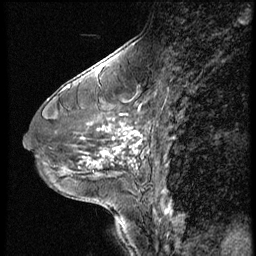
Breast MRI (dynamic contrast-enhanced), one sagittal slice. Slice 24 of 56 in the series (ordered by position). Dynamic contrast-enhanced series, image 2 of 3 at this slice position (ordered by acquisition). 1.5 T. TE 4.2 ms, TR 9 ms. 2.5 mm slice thickness. 256 × 256 image matrix, field of view 180 × 180 mm. Patient: female, 46 years. From the clinical record (not read from this slice): setting: breast cancer imaged before/during neoadjuvant chemotherapy; receptor status: HER2-positive.
Annotated regions visible in this slice (semi-automatic segmentation, software-assisted and operator-edited):
- analysis volume of interest (the breast-tissue region the enhancement analysis was run in; not a lesion): bounding box (x1, y1, x2, y2) in pixels: (64, 98, 174, 182)
- tumour enhancement mask (voxels above the 140 % enhancement threshold inside the analysis volume of interest): (88, 124, 144, 165)